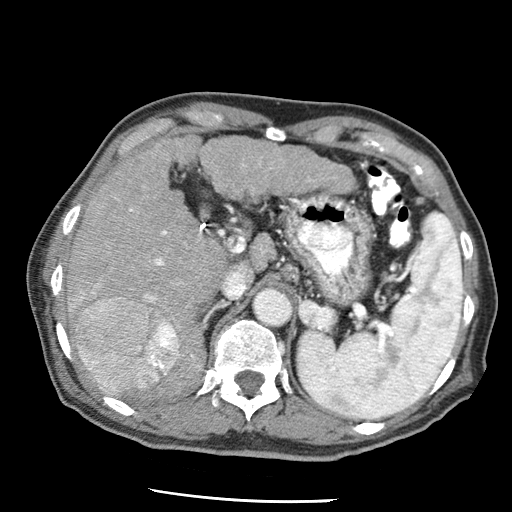
Contrast-enhanced abdominal CT (liver protocol), one axial slice. Slice 35 of 79 in the series (ordered by position). Reconstruction kernel STANDARD. Soft-tissue window (W 400 / L 40 HU). 512 × 512 image matrix, field of view 320 × 320 mm. From the clinical record (not read from this slice): diagnosis: hepatocellular carcinoma (patient treated with transarterial chemoembolisation; whether this scan precedes or follows treatment is not stated here); TNM stage (as recorded): Stage-IIIA; Child-Pugh class: A; tumour differentiation: moderately differentiated; tumour nodularity: multinodular.
Outlined on this slice (semi-automatically segmented with operator editing):
- liver parenchyma outside the tumour (the mass and vessels are separate outlines, so this box may not span the whole liver): bounding box [x1, y1, x2, y2] px = [66, 136, 354, 397]
- mass: [67, 280, 182, 389]
- liver vessels: [84, 165, 245, 392]